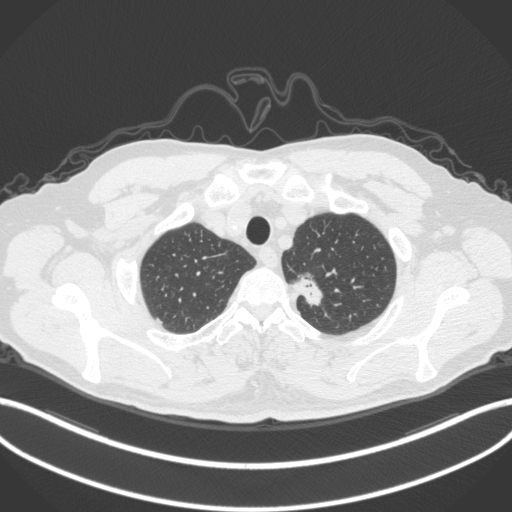
Chest CT, one axial slice. Reconstruction kernel B31f. 120 kVp. Lung window (W 1500 / L -600 HU). 1 mm slice thickness. 512 × 512 image matrix, field of view 400 × 400 mm. Male patient, age 64 years. Case-level facts recorded for this patient, not image findings: clinical TNM (as recorded): T1c N0 M0.
Annotated regions visible in this slice (rectangle marked by the reading radiologist):
- lung tumour (recorded histology: adenocarcinoma): box from (x=288, y=268) to (x=330, y=309) px